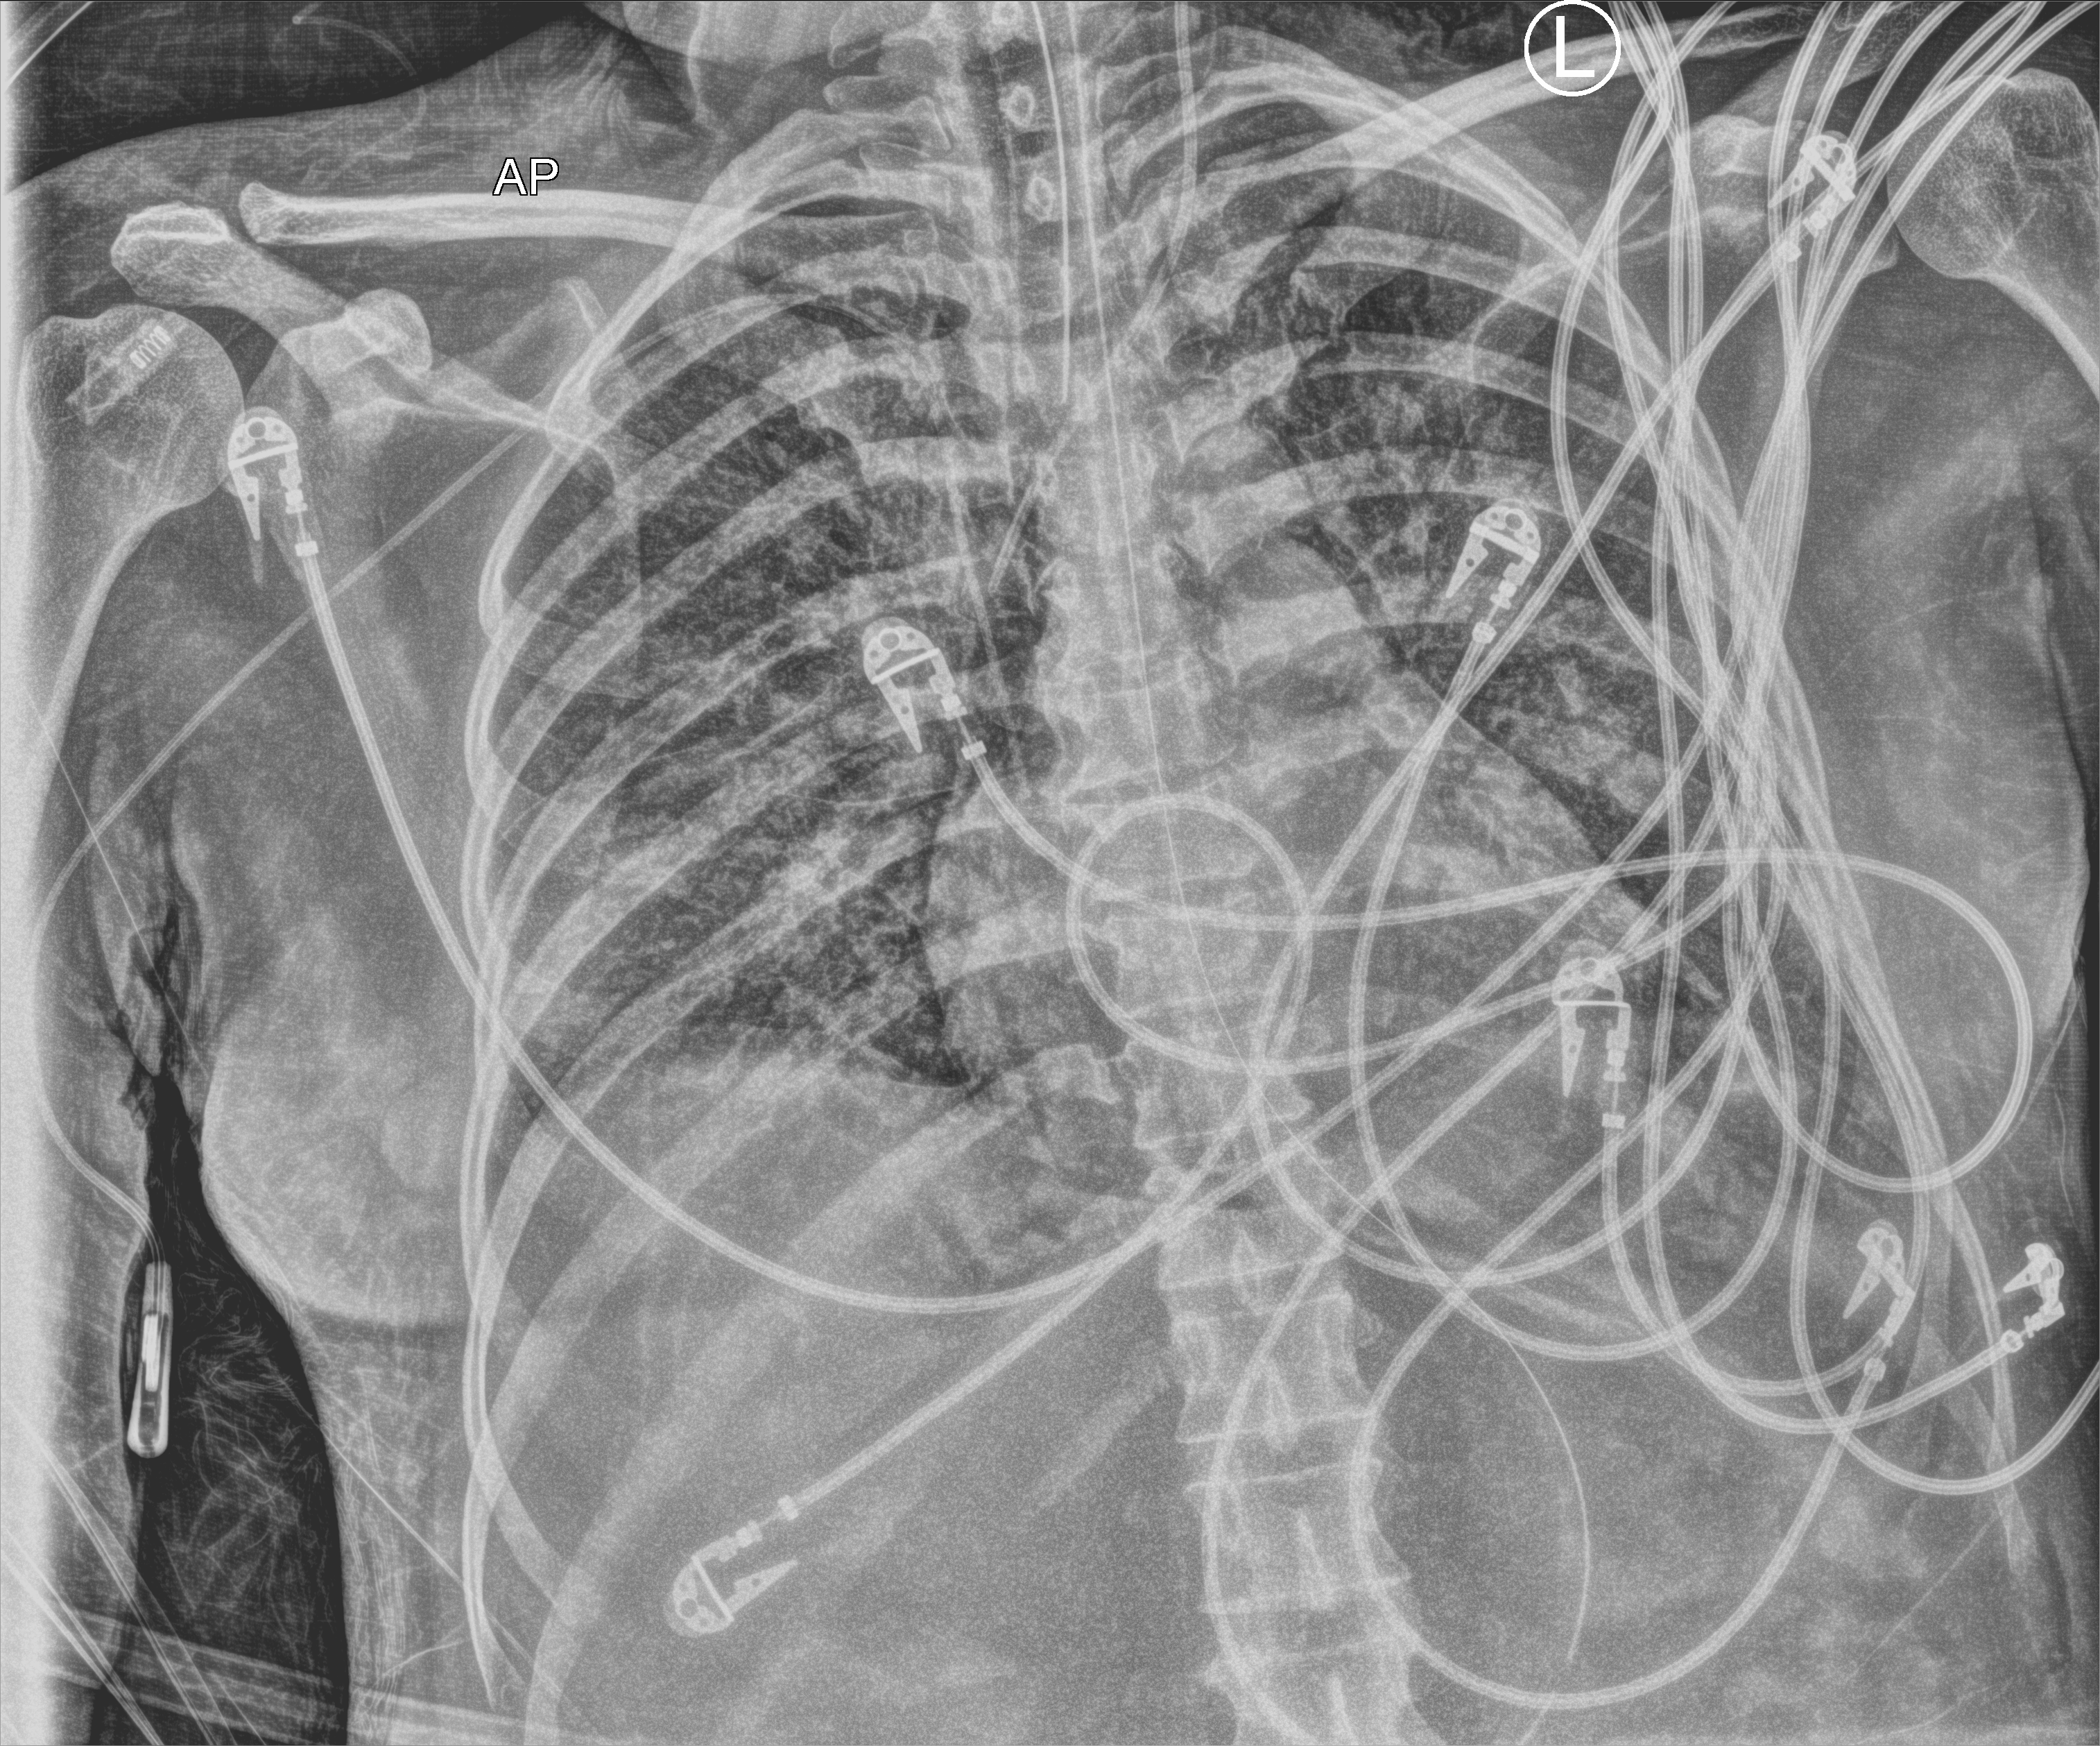
Portable chest radiograph; anteroposterior (AP) projection. Female patient hospitalised with COVID-19, age 18–59 years.
From the hospital-stay record, not from the radiograph (when in the stay this image was taken is not recorded):
- COPD (admission record): no
- mechanically ventilated during this hospital stay: yes
- admitted to intensive care during this hospital stay: yes